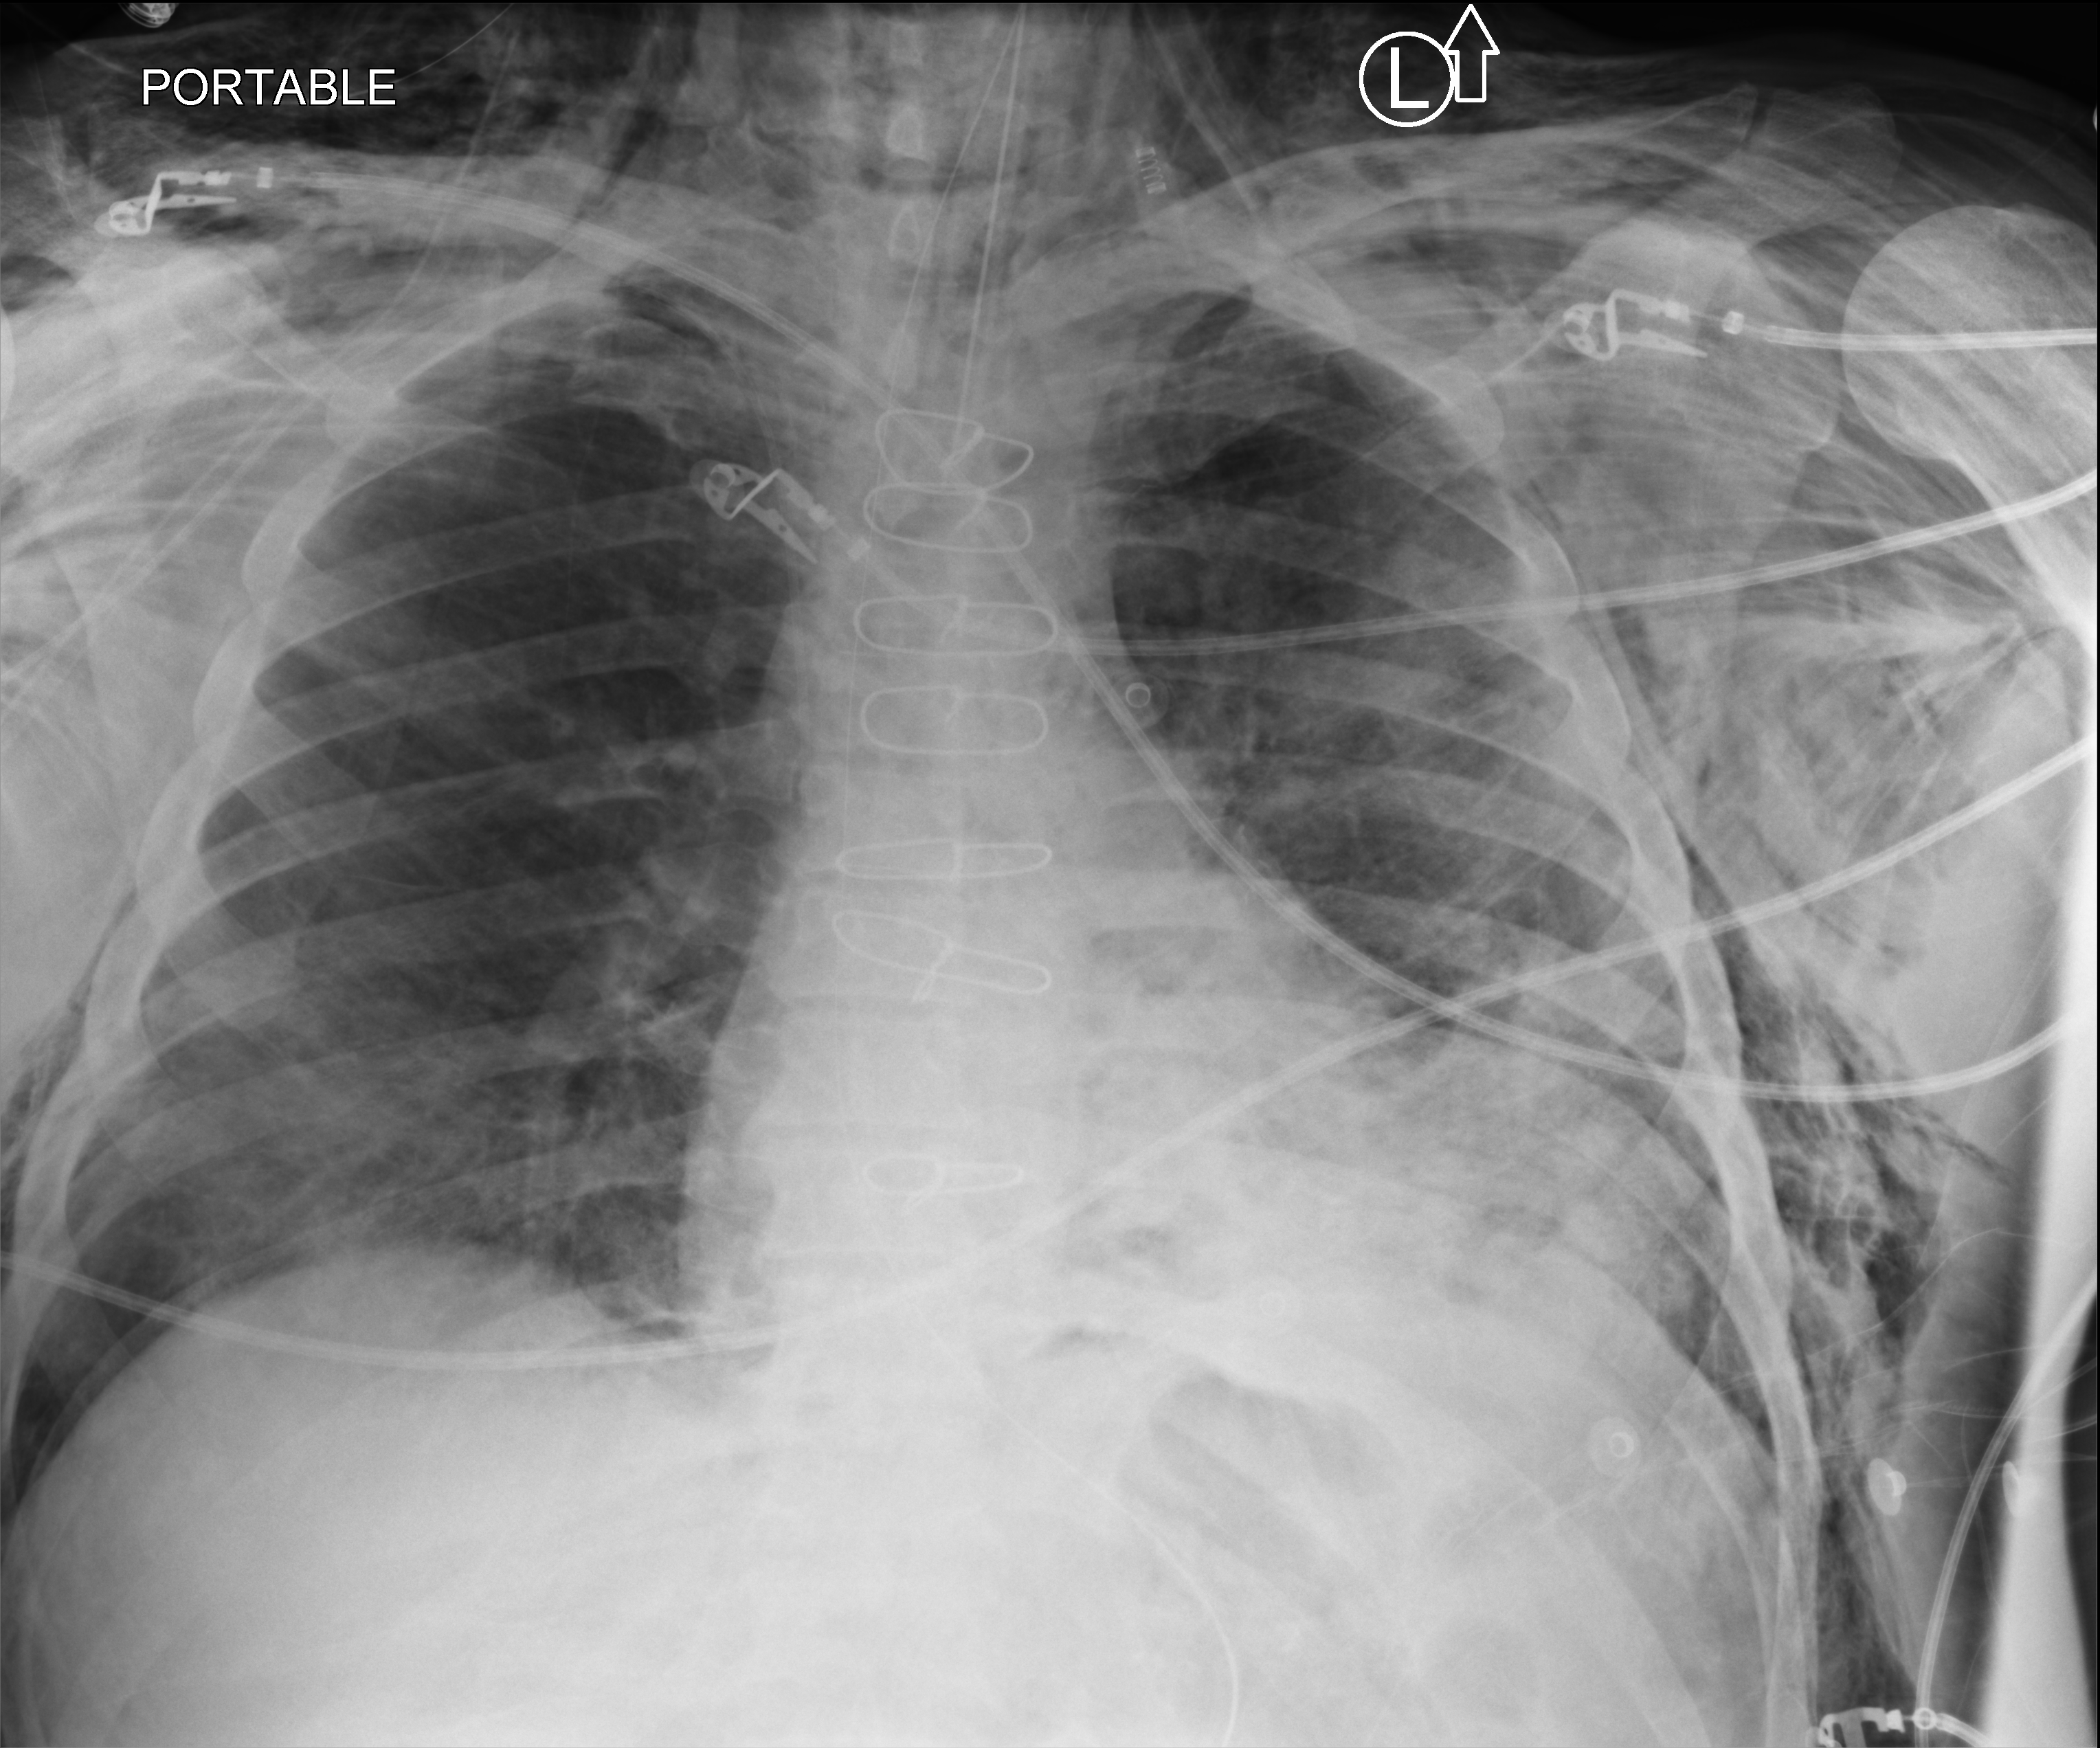
Portable chest radiograph, anteroposterior (AP) projection. Male patient hospitalised with COVID-19, age 60–74 years.
Hospital-stay facts (about this admission, not read from this image; timing relative to this image not recorded): length of hospital stay: 44 days.